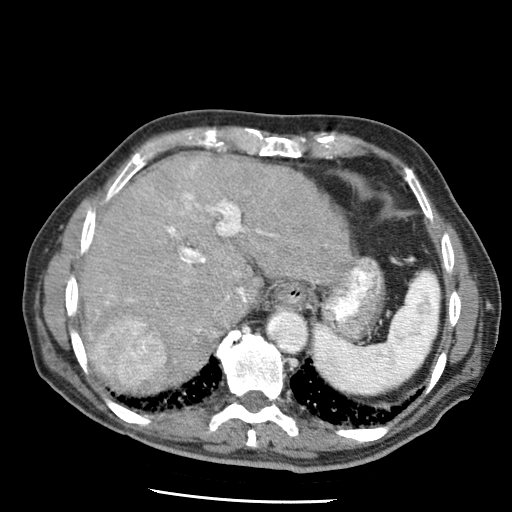
Contrast-enhanced abdominal CT (liver protocol), one axial slice. Slice 51 of 79 in the series (ordered by position). 120 kVp. Soft-tissue window (W 400 / L 40 HU). 2.5 mm slice thickness. 512 × 512 image matrix. From the clinical record (not read from this slice): diagnosis: hepatocellular carcinoma (patient treated with transarterial chemoembolisation; whether this scan precedes or follows treatment is not stated here); TNM stage (as recorded): Stage-IIIA; Child-Pugh class: A; tumour differentiation: moderately differentiated.
Outlined on this slice (semi-automatic segmentation, software-assisted and operator-edited):
- abdominal aorta: bounding box (x1, y1, x2, y2) in pixels: (269, 312, 307, 352)
- liver parenchyma outside the tumour (the mass and vessels are separate outlines, so this box may not span the whole liver): (78, 154, 348, 388)
- mass: (93, 319, 165, 383)
- liver vessels: (97, 162, 274, 341)